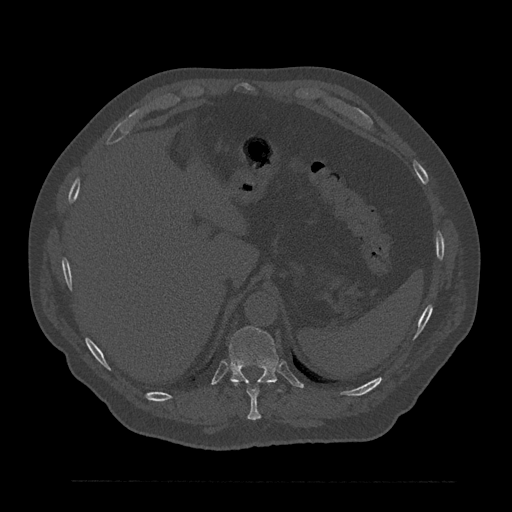
CT including the spine, one axial slice. 120 kVp. Bone window (W 1800 / L 400 HU). 0.5 mm slice thickness. 512 × 512 image matrix. Male patient, age 61 years. From the clinical record (not read from this slice): primary cancer: prostate.
Outlined on this slice (semi-automatic segmentation, software-assisted and operator-edited):
- T10 vertebra: bounding box (x1, y1, x2, y2) in pixels: (231, 381, 269, 421)
- T11 vertebra: (229, 326, 281, 391)